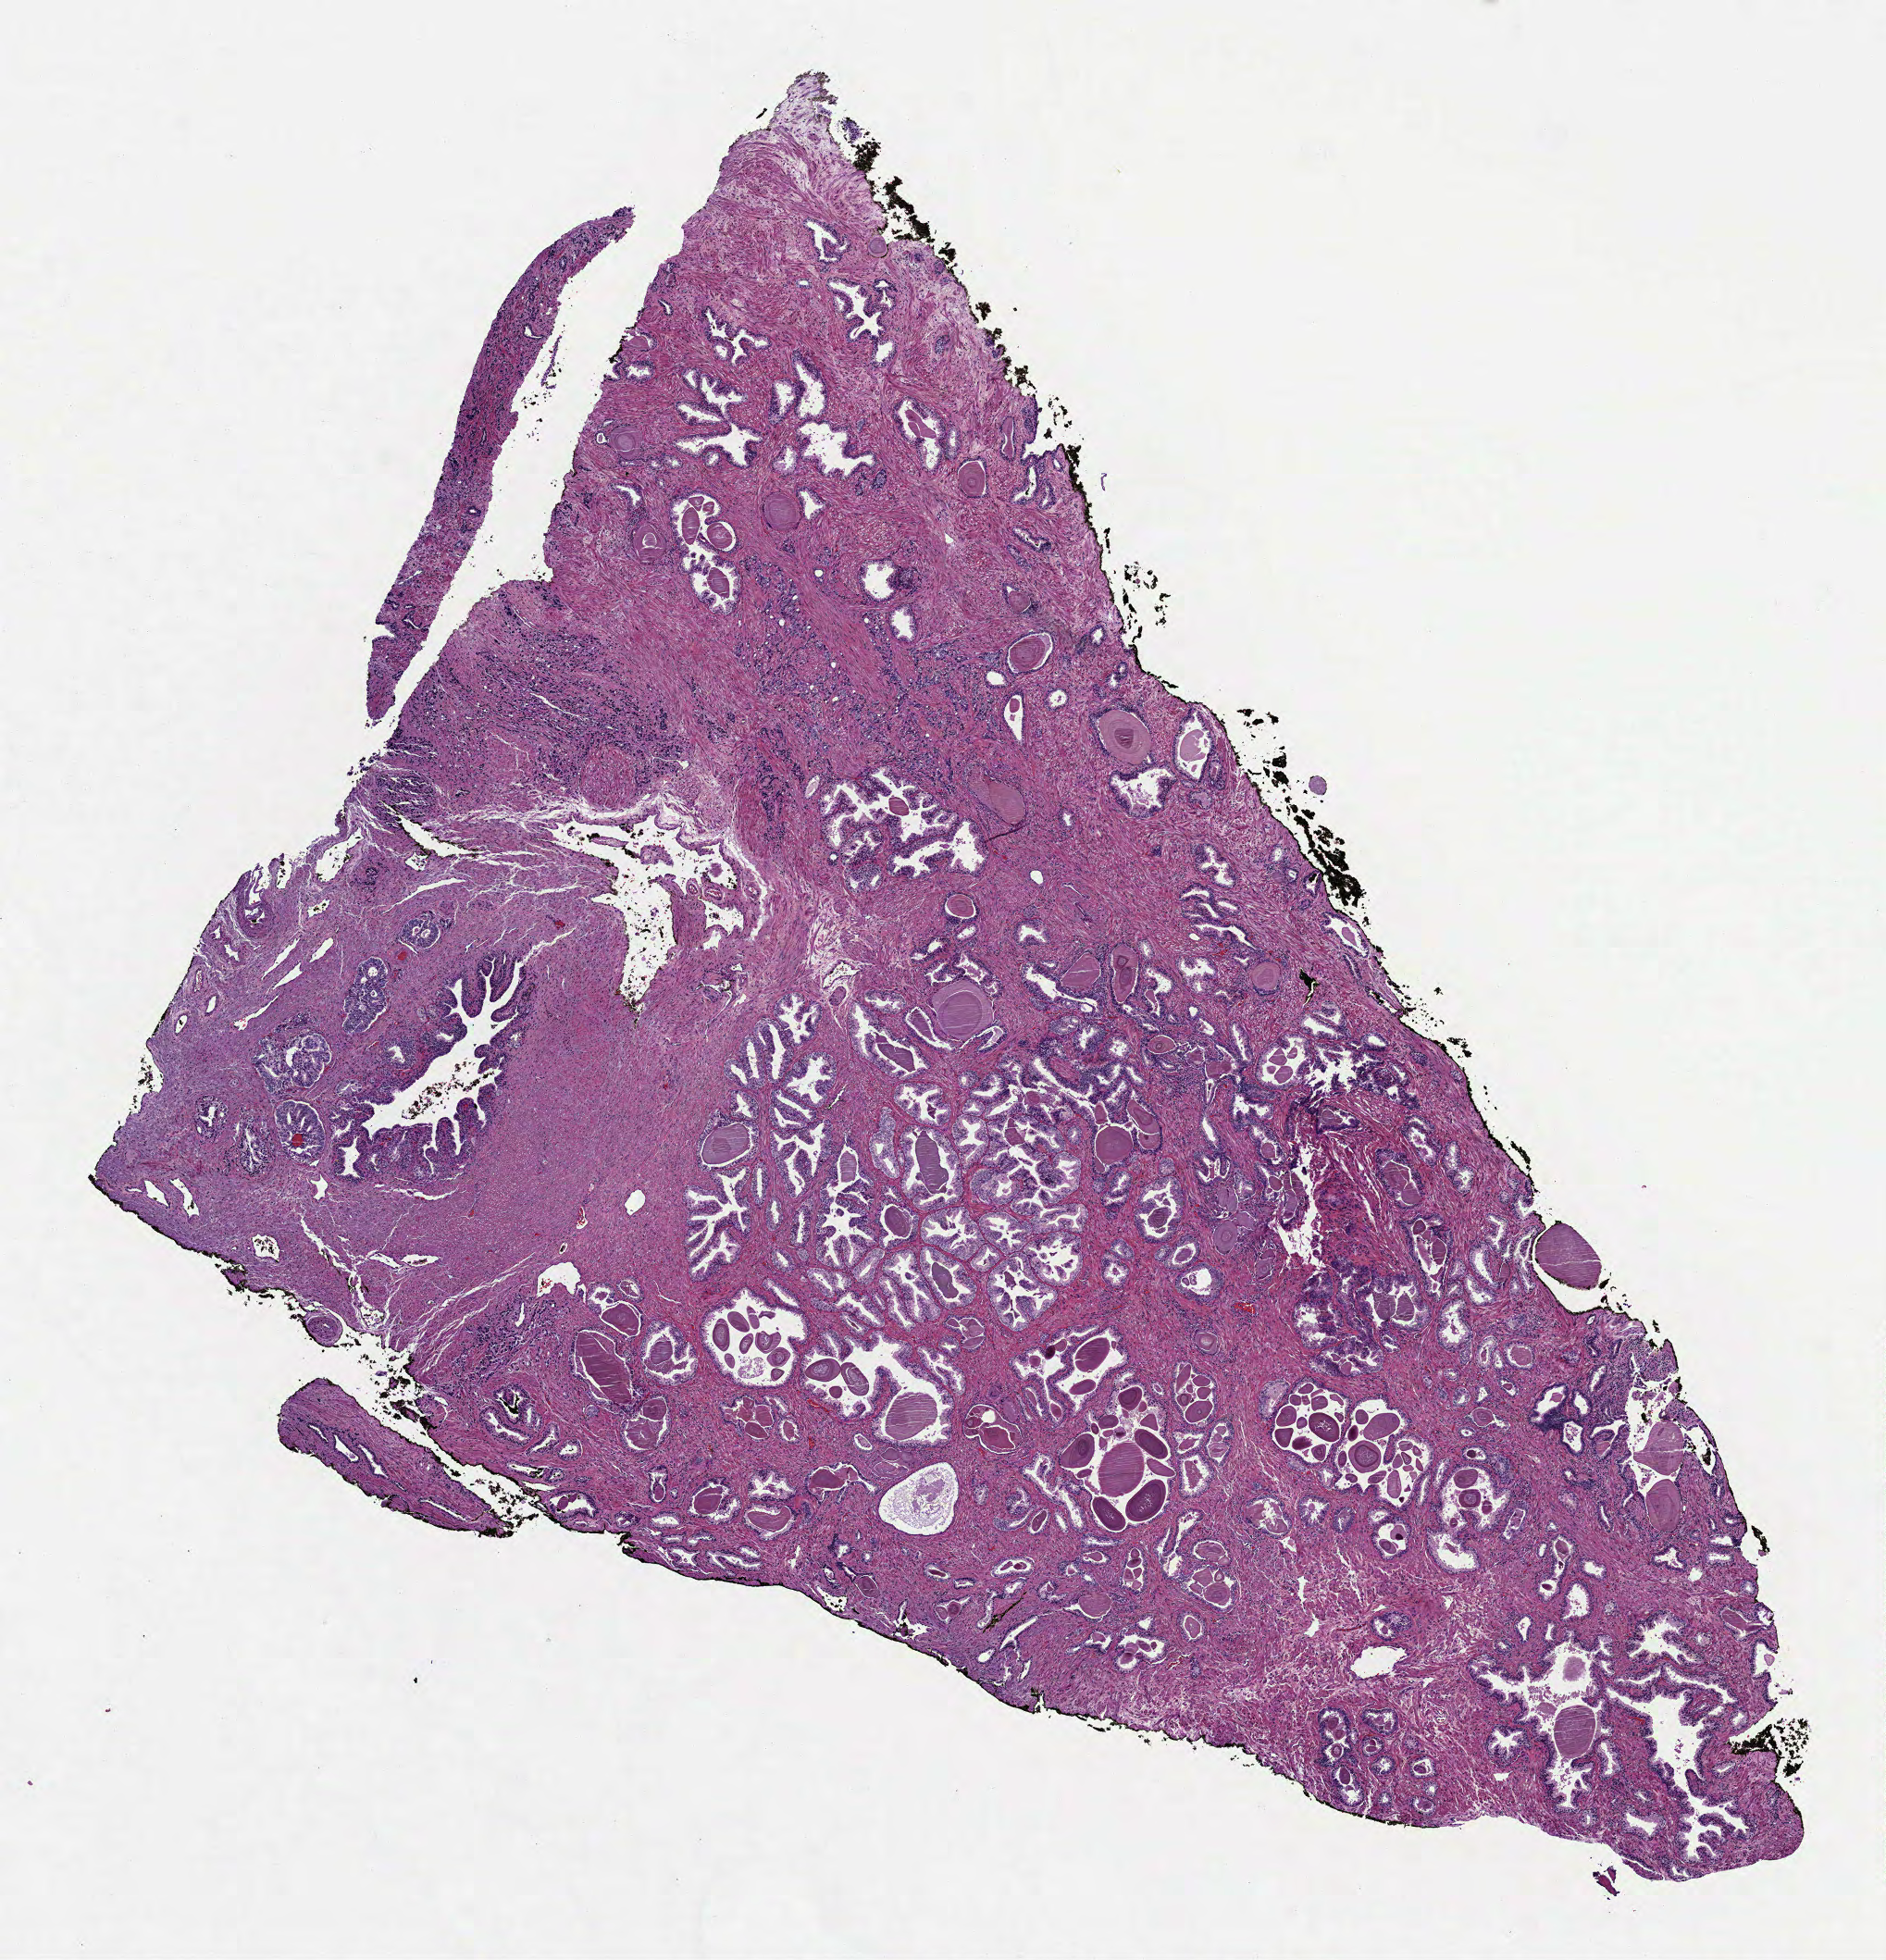
Hematoxylin and eosin (H&E) stained whole-slide image, whole scanned area (about 8.2 x 8.5 mm, acquisition: 40x scan) shown as a low-resolution overview, formalin-fixed paraffin-embedded (FFPE) diagnostic section, primary tumour sample from the prostate. Male patient; age at initial diagnosis 73 years. Gleason score: 7 (3+4).
Lymph nodes positive (case pathology): 0 of 4 examined. Pathologic diagnosis: Adenocarcinoma, NOS.